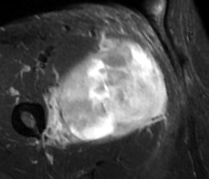
MRI of an extremity soft-tissue mass, one axial slice. Slice 45 of 89 in the series (ordered by position). STIR. MR volume resampled by the dataset authors to the PET/CT grid (not the native acquisition matrix). 3.27 mm slice thickness. 209 × 179 image matrix, field of view 204 × 175 mm. Male patient. Case-level facts recorded for this patient, not image findings: histological type: undifferentiated - pleiomorphic; grade: high; site of the primary tumour: right thigh.
Structures marked on this image (expert contour drawn on MRI and transferred to this co-registered scan by the dataset authors):
- gross tumour volume including surrounding oedema: box from (x=41, y=39) to (x=168, y=147) px
- gross tumour volume (mass): (x=55, y=39)–(x=168, y=141)